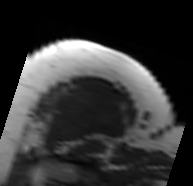
MRI of an extremity soft-tissue mass, one axial slice; slice 60 of 91 in the series (ordered by position); MR volume resampled by the dataset authors to the PET/CT grid (not the native acquisition matrix); 3.27 mm slice thickness; 193 × 186 image matrix, field of view 188 × 182 mm. Female patient. Case-level facts recorded for this patient, not image findings: histological type: malignant solitary fibrous tumor; grade: intermediate; site of the primary tumour: right thigh.
Structures marked on this image (expert contour drawn on MRI and transferred to this co-registered scan by the dataset authors):
- gross tumour volume including surrounding oedema: box from (x=42, y=85) to (x=123, y=150) px
- gross tumour volume (mass): (x=44, y=88)–(x=123, y=148)